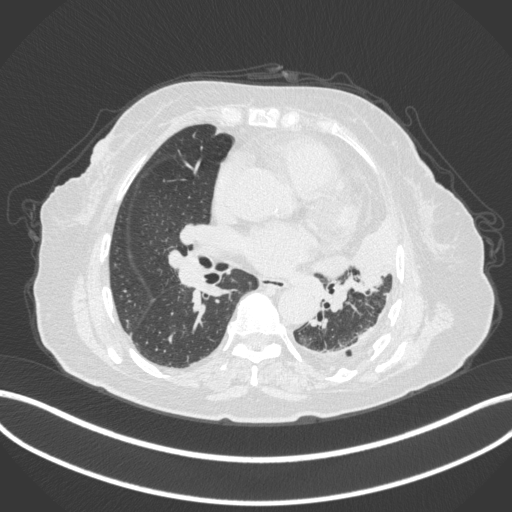
Chest CT, one axial slice; 120 kVp; lung window (W 1500 / L -600 HU); 1 mm slice thickness; 512 × 512 image matrix, field of view 400 × 400 mm. Female patient, age 75 years. From the clinical record (not read from this slice): clinical TNM (as recorded): T3 N3 M1.
Outlined on this slice (rectangle marked by the reading radiologist):
- lung tumour (recorded histology: adenocarcinoma): bounding box (x1, y1, x2, y2) in pixels: (314, 218, 393, 291)